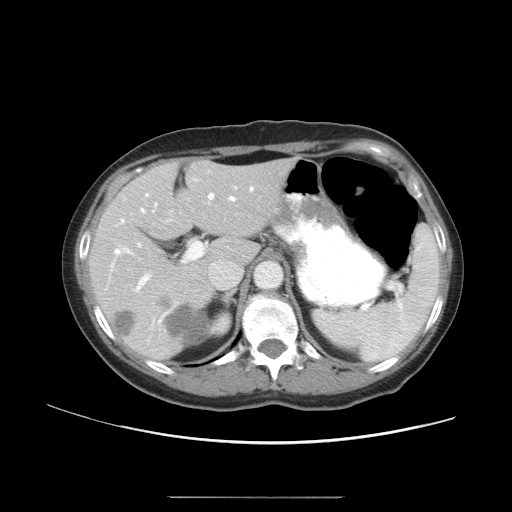
Contrast-enhanced abdominal CT, one axial slice. Slice 31 of 50 in the series (ordered by position). Reconstruction kernel STANDARD. 120 kVp. Soft-tissue window (W 400 / L 40 HU). 5 mm slice thickness. 512 × 512 image matrix, field of view 389 × 389 mm. Female patient, age 58 years. Case-level facts recorded for this patient, not image findings: diagnosis: colorectal cancer liver metastases, imaged before liver resection; multiple liver metastases: yes; largest metastasis: 7.3 cm; disease in both lobes: yes.
Annotated regions visible in this slice (outlined manually by an expert reader):
- hepatic veins: bounding box [x1, y1, x2, y2] px = [115, 187, 253, 254]
- liver: [91, 161, 288, 360]
- planned liver remnant (the part of the liver to remain after resection): [174, 161, 288, 261]
- portal vein (with intrahepatic branches): [123, 192, 215, 291]
- liver metastasis: [166, 307, 203, 344]
- liver metastasis: [113, 313, 136, 336]